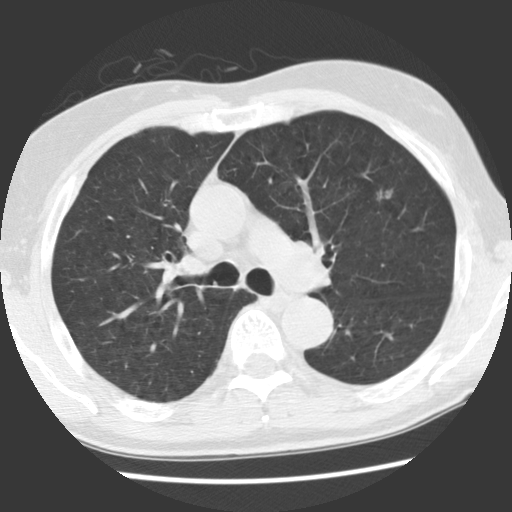
Axial slice from a low-dose chest CT screening exam, baseline screening round, lung window (W 1500 / L -600 HU), 2.5 mm slice thickness, standard (soft-tissue) reconstruction kernel (STANDARD), 140 kVp, slice 84 of 131 in the series, 512 × 512 image matrix, field of view 320 × 320 mm. Male, age 70 years at enrolment. Current smoker at enrolment.
Lesion marked by an expert reader, bounding box (x1, y1, x2, y2) in pixels: (355, 180, 404, 224). The screening reader recorded 2 non-calcified nodules or masses ≥4 mm on this exam (left upper lobe, right lower lobe); which of them this box marks is not recorded. Official screen result: positive, change unspecified: nodule(s) >= 4 mm or enlarging nodule(s), mass(es), or other non-specific abnormalities suspicious for lung cancer. Later outcome: lung cancer diagnosed 879 days after this screen — adenocarcinoma, NOS, left upper lobe, moderately differentiated (G2), stage IIIA (AJCC 6th edition), 17 mm at pathology.